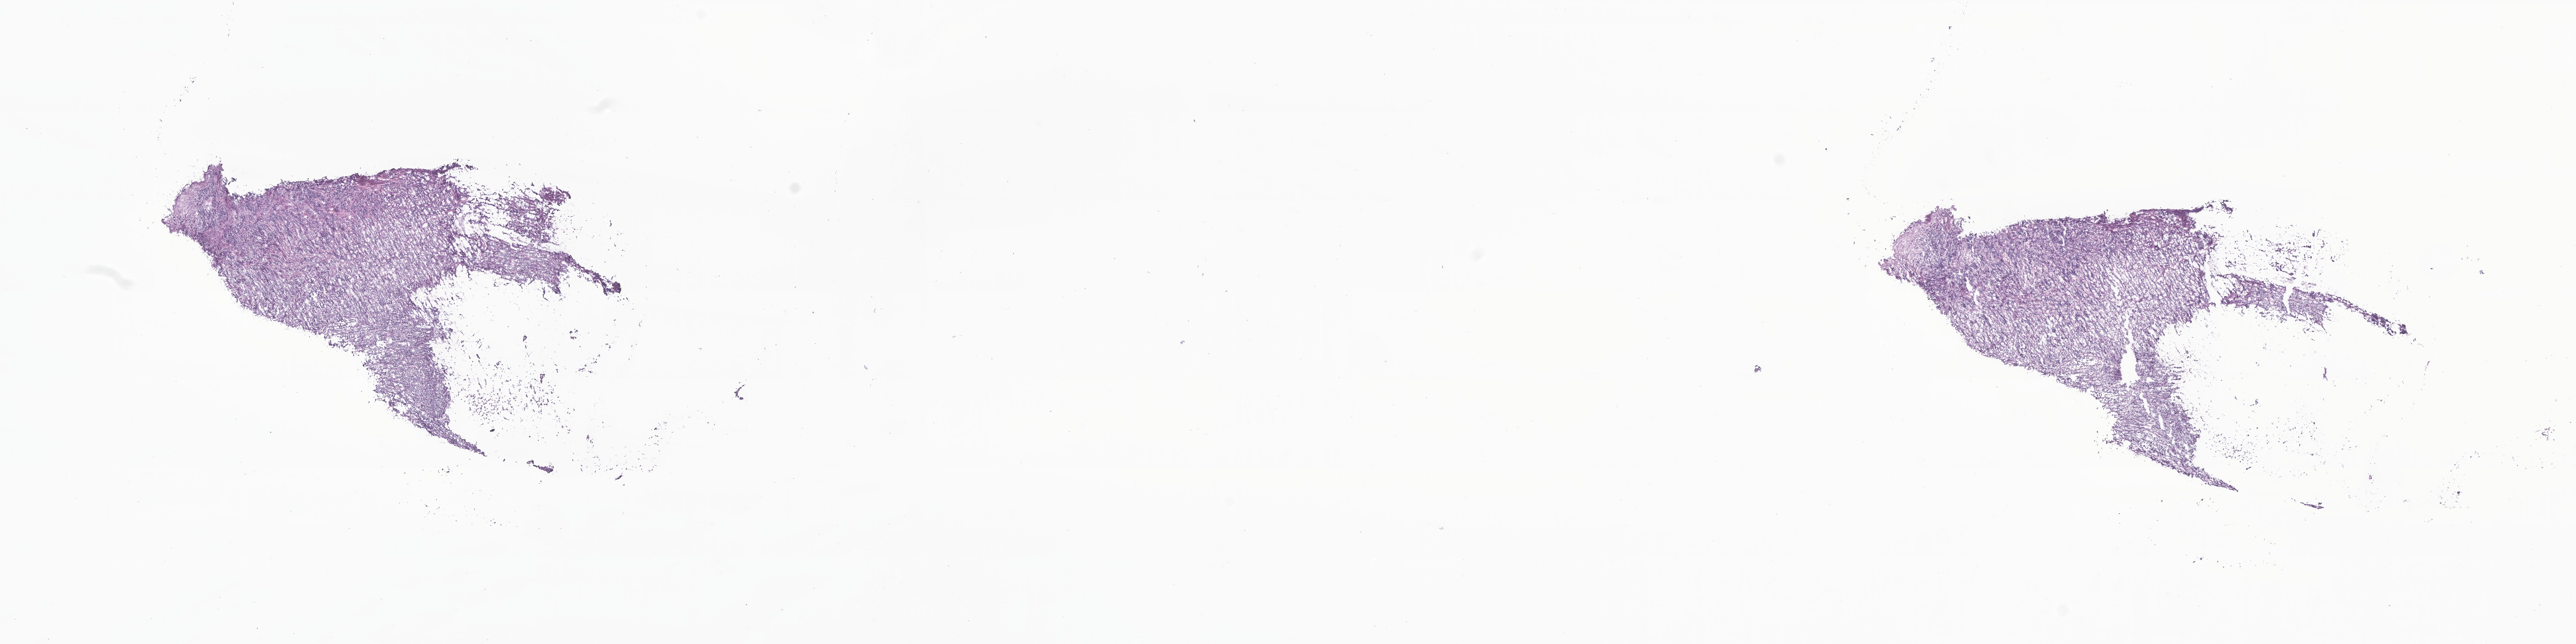
Hematoxylin and eosin (H&E) whole-slide image of tumor tissue from the brain — a low-resolution overview of the entire scanned area, about 31.0 x 7.7 mm, cryosection (OCT / tissue freezing medium). Patient male; age 107 months (8 years 11 months).
Diagnosis: Medulloblastoma, NOS.